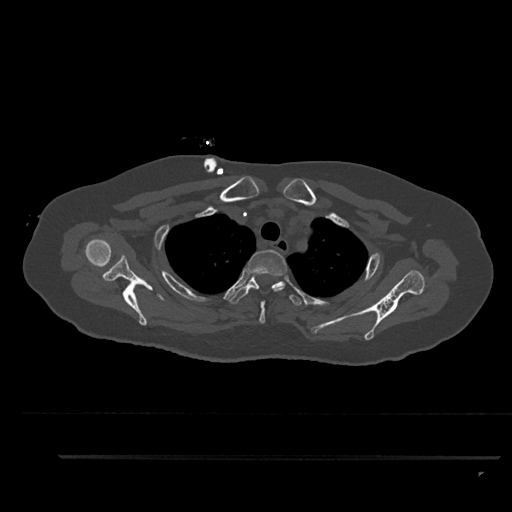
CT including the spine, one axial slice; 120 kVp; bone window (W 1800 / L 400 HU); 0.5 mm slice thickness; 512 × 512 image matrix, field of view 408 × 408 mm. Female patient, age 44 years. Case-level facts recorded for this patient, not image findings: primary cancer: renal.
Outlined on this slice (semi-automatic segmentation, software-assisted and operator-edited):
- T1 vertebra: box from (x=282, y=284) to (x=284, y=286) px
- T2 vertebra: (x=247, y=250)–(x=287, y=324)
- T3 vertebra: (x=229, y=273)–(x=304, y=306)